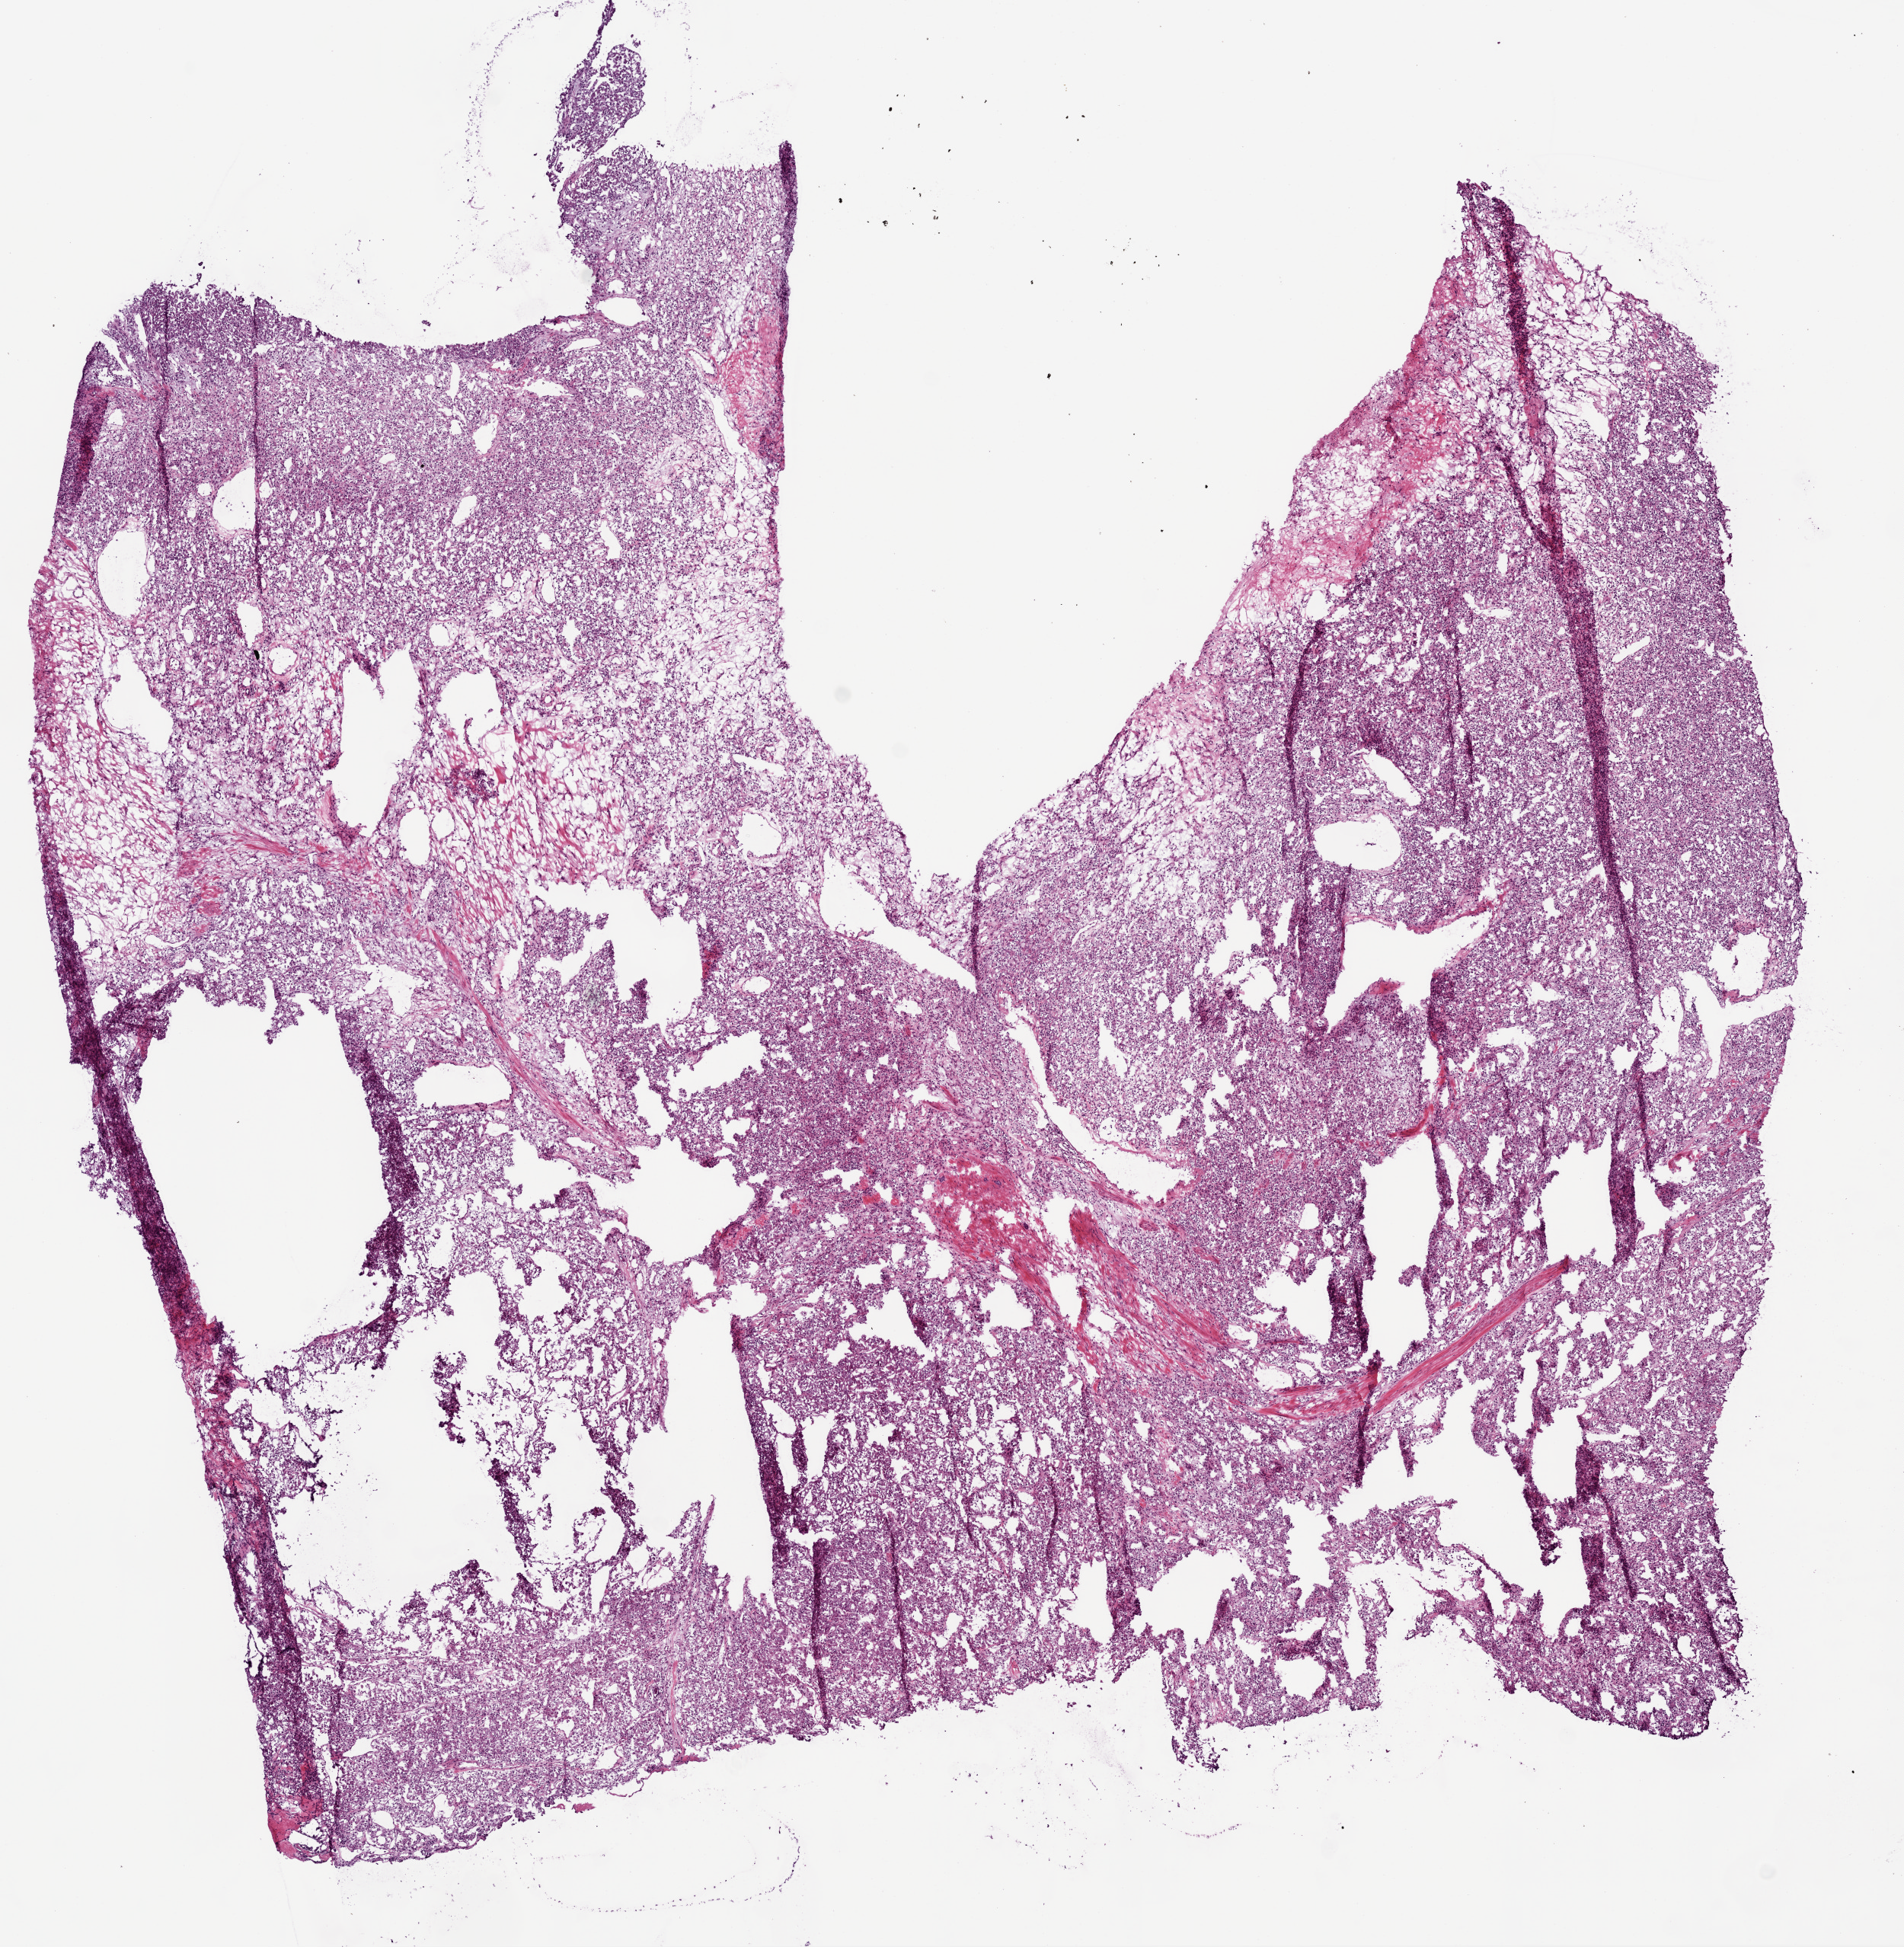
Whole-slide histology image, H&E-stained, low-resolution overview of the scanned area, about 10.0 x 10.3 mm (acquisition: 20x scan), frozen section from the top of the tissue portion, kidney, primary tumour sample. Male patient; age at initial diagnosis 69 years. Histologic grade: G4 (undifferentiated). Composition of this section per pathologist review: tumour cells 90%, tumour nuclei 85%, normal cells 0%, stromal cells 10%, necrosis 0%.
AJCC pathologic stage: III. Pathologic diagnosis: Clear cell adenocarcinoma, NOS.